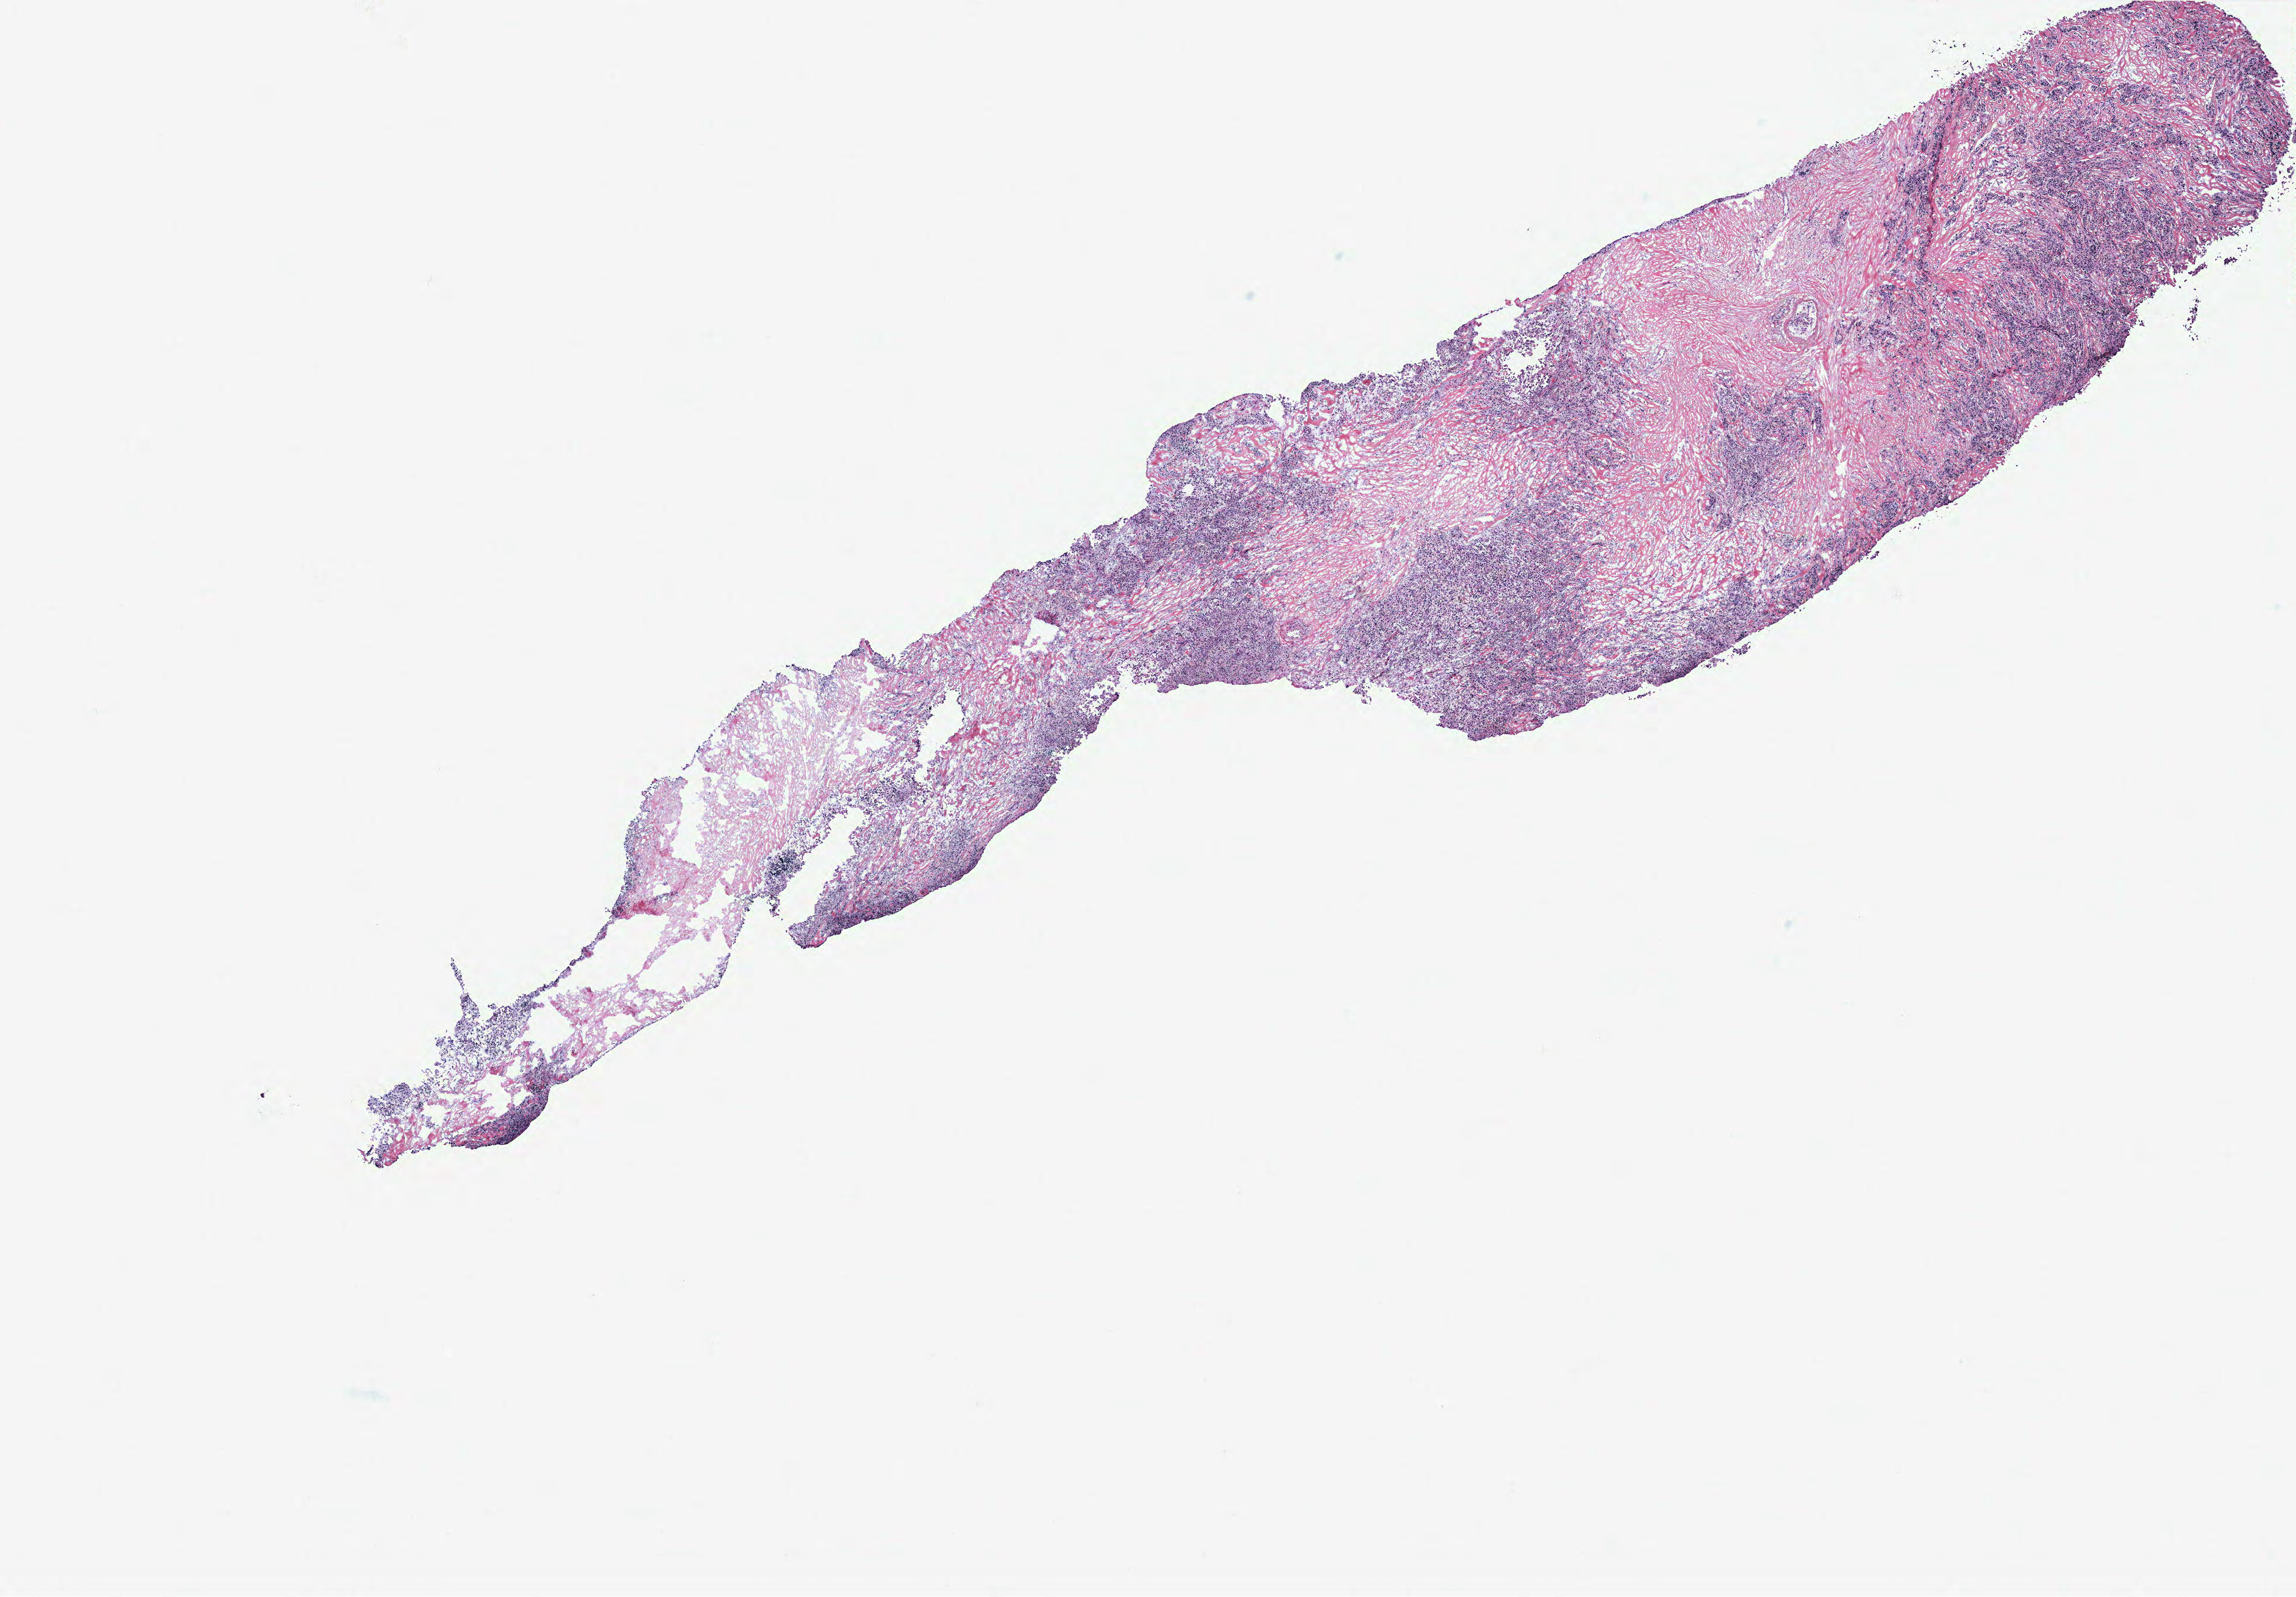
H&E-stained whole-slide image, a low-resolution overview of the entire scanned area, about 15.6 x 10.9 mm (from a 40x scan). Breast, tumour tissue. Female, 84 y/o.
AJCC pathologic stage: IIIA. Histologic diagnosis: Infiltrating duct carcinoma, NOS.